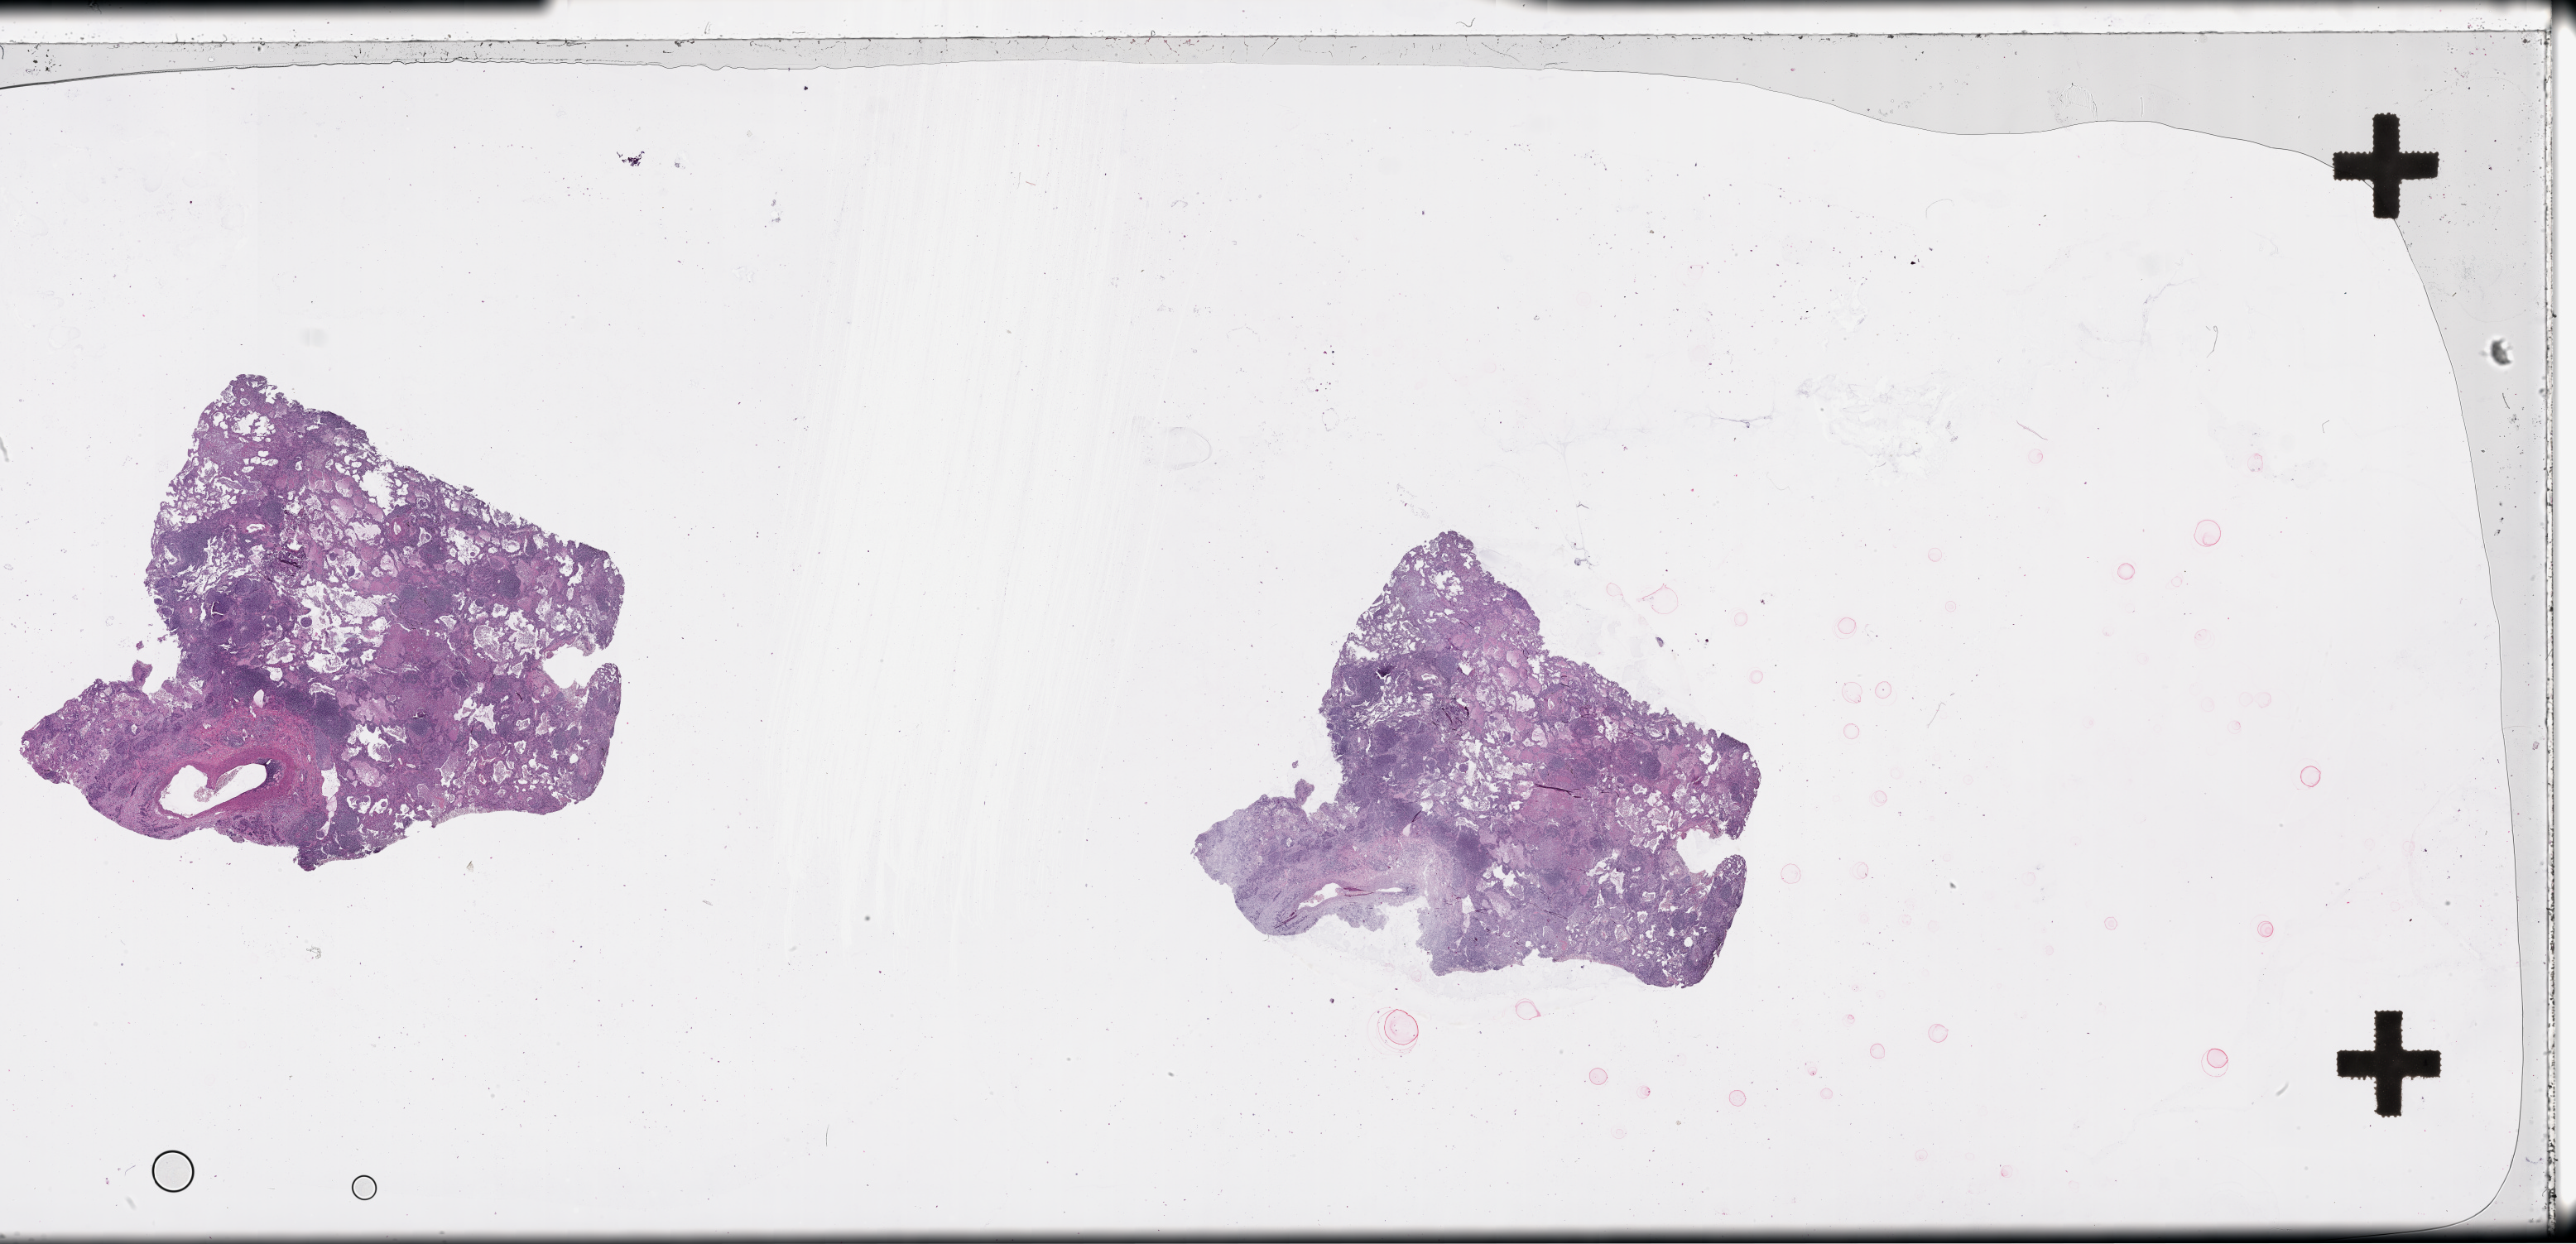
Whole-slide histology image, H&E — whole scanned area (about 50.1 x 24.2 mm) shown as a low-resolution overview; lung, tumour tissue. Patient: female, age 58 years.
Patient diagnosis (cohort enrolment): squamous cell carcinoma (lung).